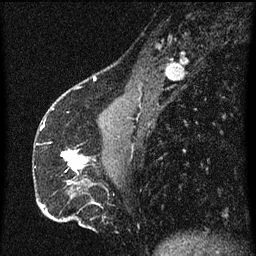
Breast MRI (dynamic contrast-enhanced), one sagittal slice; position 22 of 60 along the scan axis; dynamic contrast-enhanced series, image 2 of 3 at this slice position (ordered by acquisition); 1.5 T; TE 4.2 ms, TR 8 ms; 256 × 256 image matrix, field of view 180 × 180 mm. Female patient, age 51 years.
Outlined on this slice (semi-automatic segmentation, software-assisted and operator-edited):
- analysis volume of interest (the breast-tissue region the enhancement analysis was run in; not a lesion): bounding box [x1, y1, x2, y2] px = [62, 150, 89, 175]
- tumour enhancement mask (voxels above the 70 % enhancement threshold inside the analysis volume of interest): [62, 150, 89, 173]